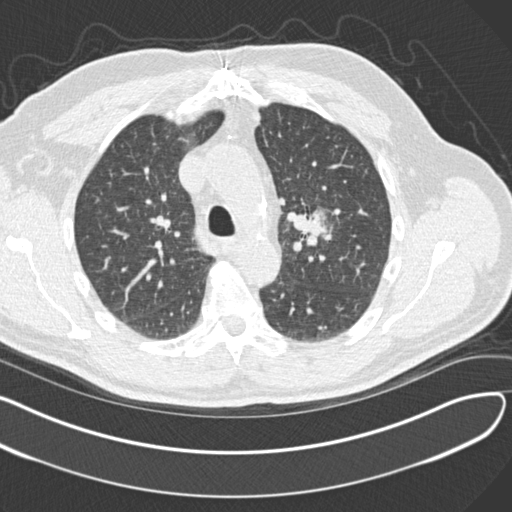
Low-dose screening chest CT, axial slice; second annual screen; lung window (W 1500 / L -600 HU); 2 mm slice thickness; standard (soft-tissue) reconstruction kernel (B30f); 512 × 512 image matrix, field of view 372 × 372 mm. Male, age 65 years at enrolment. Former smoker at enrolment.
Expert-annotated lung lesion, box from (x=286, y=196) to (x=344, y=258) px. The screening reader recorded 4 non-calcified nodules or masses ≥4 mm on this exam; which of them this box marks is not recorded. Official screen result: positive, other. Later outcome: lung cancer diagnosed 577 days after this screen — acinar cell carcinoma, left upper lobe, stage IA (AJCC 6th edition), 25 mm at pathology.